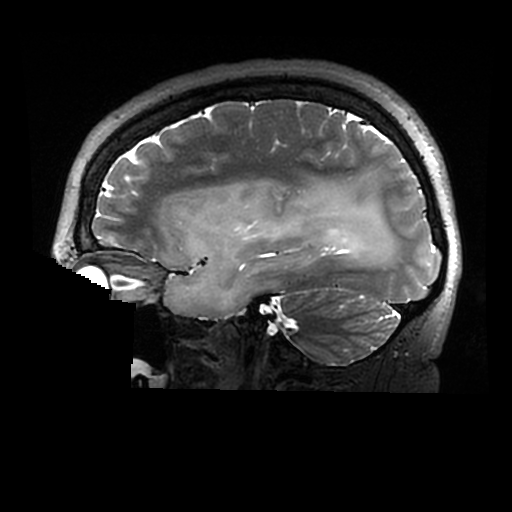
Brain MRI from a brain-tumour surgery series, one sagittal slice. Slice 201 of 320 in the series (ordered by position). 512 × 512 image matrix. Case-level facts recorded for this patient, not image findings: histopathology: Astrocytoma; WHO grade: 2; IDH mutation: yes.
Structures marked on this image (manually delineated by an expert):
- tumour: bounding box [x1, y1, x2, y2] px = [162, 181, 397, 318]